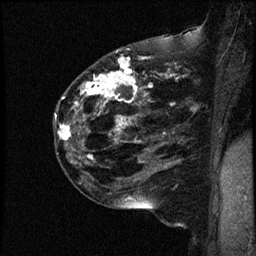
Breast MRI (dynamic contrast-enhanced), one sagittal slice; slice 31 of 44 in the series (ordered by position); dynamic contrast-enhanced study with each time point stored as its own series, time point 2 of 4 at this slice position (early post-contrast, ordered by acquisition time); 1.5 T; TE 4.2 ms, TR 17.7 ms; 256 × 256 image matrix, field of view 200 × 200 mm. Female patient, age 52 years. Case-level facts recorded for this patient, not image findings: setting: breast cancer imaged before/during neoadjuvant chemotherapy; receptor status: HR-positive, HER2-negative.
Annotated regions visible in this slice (semi-automatically segmented with operator editing):
- analysis volume of interest (the breast-tissue region the enhancement analysis was run in; not a lesion): bounding box <53,48,163,147> (left, top, right, bottom; pixels)
- tumour enhancement mask (voxels above the 100 % enhancement threshold inside the analysis volume of interest): <57,51,152,143>